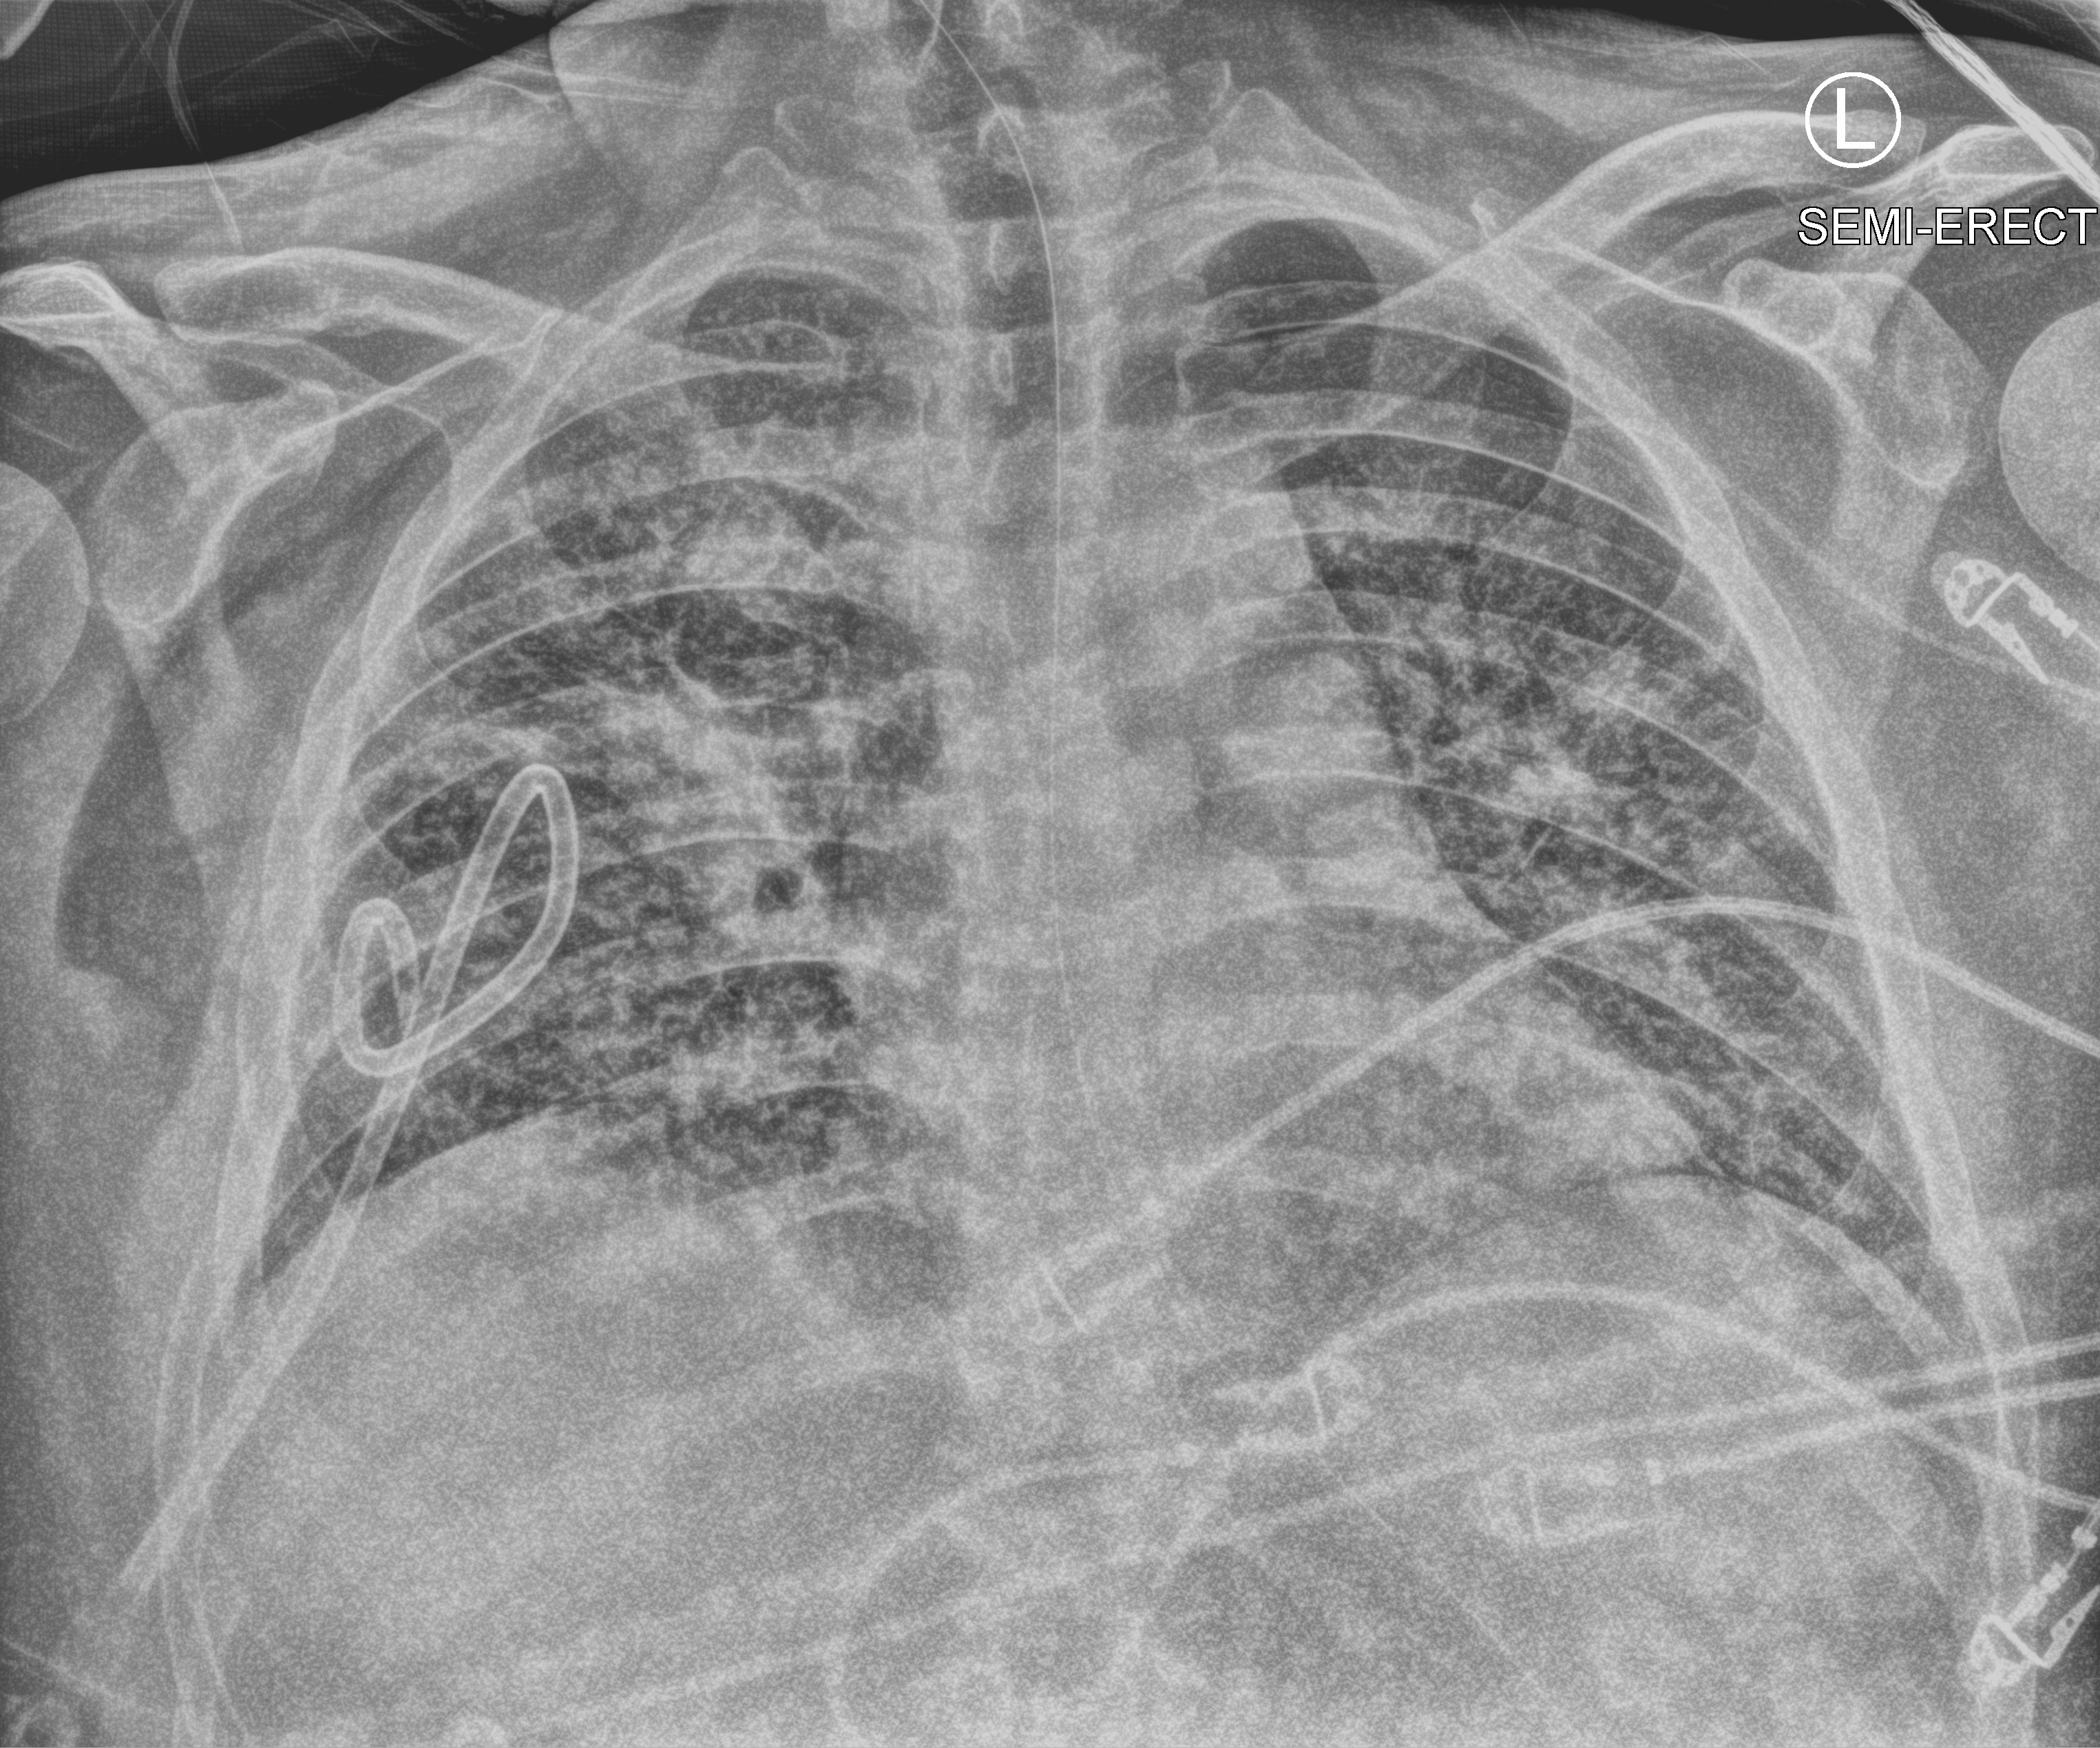
Portable chest radiograph. Patient hospitalised with COVID-19, aged 18–59 years.
Hospital-stay facts (about this admission, not read from this image; timing relative to this image not recorded): length of hospital stay: 31 days.